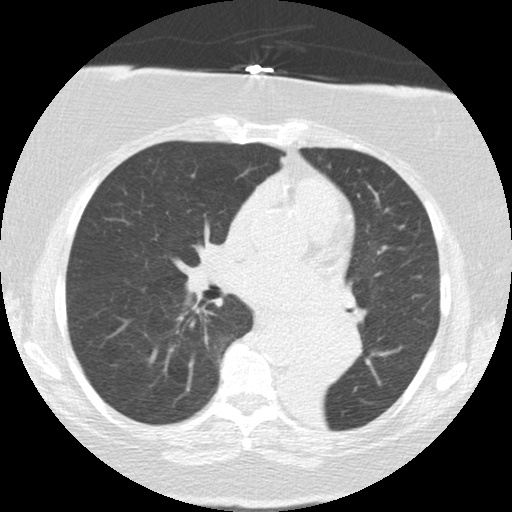
Low-dose screening chest CT, axial slice. Baseline annual screen. Lung window (W 1500 / L -600 HU). 2.5 mm slice thickness. Standard (soft-tissue) reconstruction kernel (STANDARD). Slice 64 of 136 in the series. Female participant, aged 71 years at enrolment.
Expert-annotated lung lesion, bounding box [x1, y1, x2, y2] px = [286, 307, 364, 383]. Reader record for this screening exam (exam-level; its link to the box is not recorded): non-calcified nodule or mass ≥4 mm, right middle lobe, 5 × 5 mm, smooth margins, soft tissue attenuation. Note: the box lies in the patient's left hemithorax on this image, whereas the reader's record names the right lung; they may be different findings. Participant outcome: lung cancer diagnosed 46 days after this screen — large cell carcinoma, NOS, left lower lobe, mediastinum, other location, poorly differentiated (G3), stage IV (AJCC 6th edition), 50 mm at pathology.